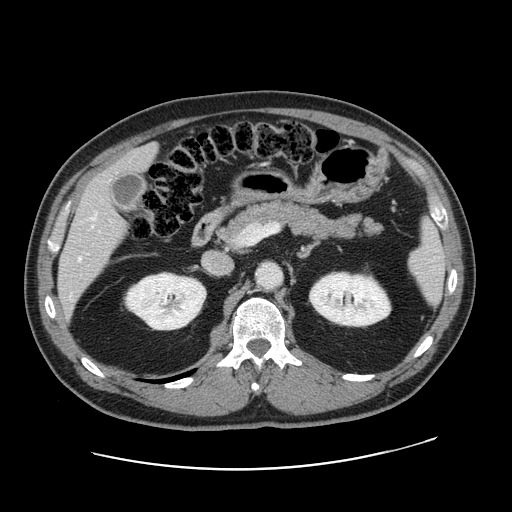
Contrast-enhanced abdominal CT, one axial slice; slice 86 of 178 in the series (ordered by position); intravenous contrast given; soft-tissue window (W 400 / L 40 HU); 512 × 512 image matrix, field of view 403 × 403 mm. Male patient, age 63 years. Case-level facts recorded for this patient, not image findings: diagnosis: colorectal cancer liver metastases, imaged before liver resection; multiple liver metastases: yes; largest metastasis: 8 cm; disease in both lobes: yes.
Annotated regions visible in this slice (manually delineated by an expert):
- hepatic veins: bounding box (x1, y1, x2, y2) in pixels: (78, 214, 96, 260)
- liver: (59, 146, 156, 309)
- planned liver remnant (the part of the liver to remain after resection): (112, 146, 156, 173)